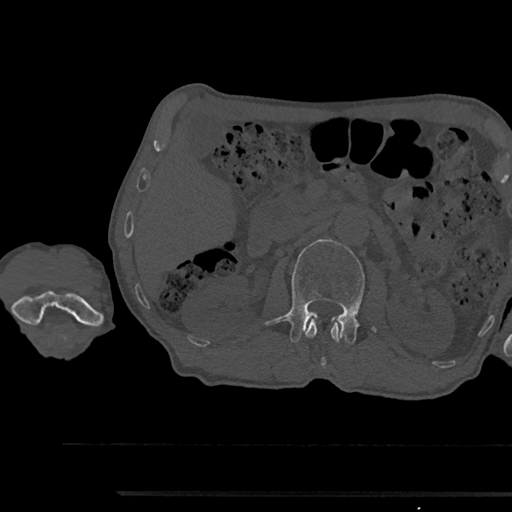
CT including the spine, one axial slice; slice 590 of 797 in the series (ordered by position); 120 kVp; bone window (W 1800 / L 400 HU); 0.5 mm slice thickness; 512 × 512 image matrix, field of view 367 × 367 mm. Patient: male, 79 years. From the clinical record (not read from this slice): primary cancer: prostate.
Structures marked on this image (semi-automatic segmentation, software-assisted and operator-edited):
- L1 vertebra: box from (x=305, y=319) to (x=341, y=366) px
- L2 vertebra: (x=264, y=239)–(x=376, y=344)